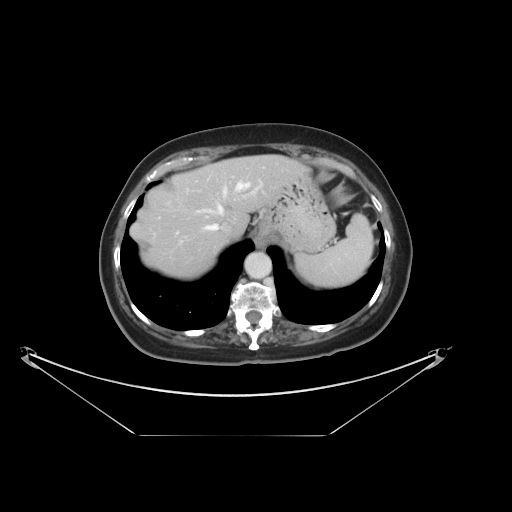
Contrast-enhanced abdominal CT, one axial slice; position 29 of 36 along the scan axis; reconstruction kernel STANDARD; intravenous contrast given; soft-tissue window (W 400 / L 40 HU); 5 mm slice thickness; 512 × 512 image matrix. Female patient, age 70 years. Case-level facts recorded for this patient, not image findings: diagnosis: colorectal cancer liver metastases, imaged before liver resection; multiple liver metastases: no; largest metastasis: 2.5 cm.
Annotated regions visible in this slice (outlined manually by an expert reader):
- hepatic veins: box from (x=205, y=183) to (x=249, y=231) px
- liver: (x=131, y=156)–(x=301, y=278)
- planned liver remnant (the part of the liver to remain after resection): (x=131, y=156)–(x=301, y=278)
- portal vein (with intrahepatic branches): (x=177, y=180)–(x=263, y=233)